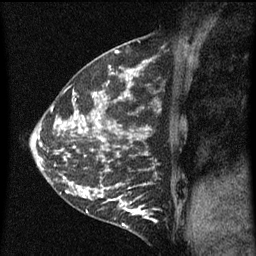
Breast MRI (dynamic contrast-enhanced), one sagittal slice; position 19 of 60 along the scan axis; dynamic contrast-enhanced series, image 2 of 5 at this slice position (ordered by acquisition); 1.5 T; TE 4.2 ms, TR 8 ms; 256 × 256 image matrix, field of view 180 × 180 mm. Patient: female, 35 years.
Structures marked on this image (semi-automatically segmented with operator editing):
- analysis volume of interest (the breast-tissue region the enhancement analysis was run in; not a lesion): bounding box <118,196,158,229> (left, top, right, bottom; pixels)
- tumour enhancement mask (voxels above the 70 % enhancement threshold inside the analysis volume of interest): <120,196,158,223>